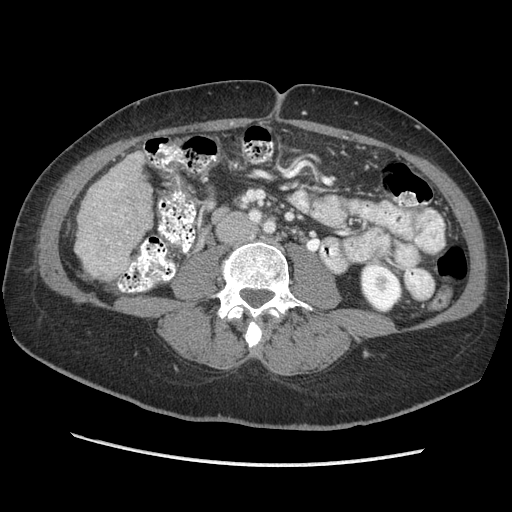
Contrast-enhanced abdominal CT (liver protocol), one axial slice. Slice 90 of 170 in the series (ordered by position). Reconstruction kernel STANDARD. 140 kVp. Soft-tissue window (W 400 / L 40 HU). 512 × 512 image matrix. Case-level facts recorded for this patient, not image findings: diagnosis: hepatocellular carcinoma (patient treated with transarterial chemoembolisation; whether this scan precedes or follows treatment is not stated here); TNM stage (as recorded): Stage-II; Child-Pugh class: A; tumour differentiation: no biopsy; tumour nodularity: multinodular.
Structures marked on this image (semi-automatic segmentation, software-assisted and operator-edited):
- liver parenchyma outside the tumour (the mass and vessels are separate outlines, so this box may not span the whole liver): bounding box <75,151,152,278> (left, top, right, bottom; pixels)
- liver vessels: <106,184,122,261>